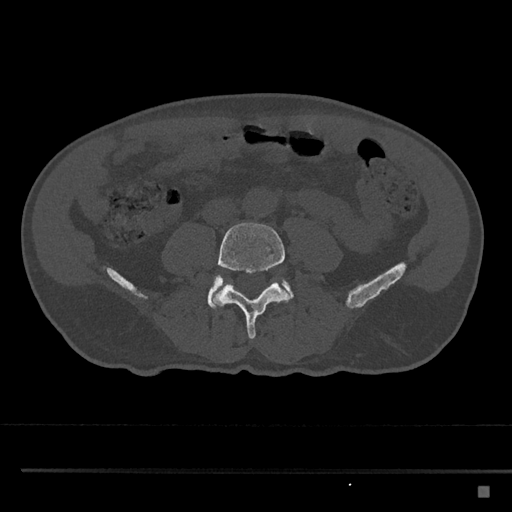
CT including the spine, one axial slice. Slice 626 of 797 in the series (ordered by position). Bone window (W 1800 / L 400 HU). 0.5 mm slice thickness. 512 × 512 image matrix, field of view 391 × 391 mm. Patient: male, 59 years. Case-level facts recorded for this patient, not image findings: primary cancer: prostate.
Annotated regions visible in this slice (semi-automatic segmentation, software-assisted and operator-edited):
- L4 vertebra: bounding box (x1, y1, x2, y2) in pixels: (212, 222, 290, 339)
- L5 vertebra: (207, 275, 294, 309)